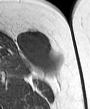
MRI of an extremity soft-tissue mass, one axial slice. Slice 21 of 45 in the series (ordered by position). MR volume resampled by the dataset authors to the PET/CT grid (not the native acquisition matrix). 90 × 109 image matrix, field of view 88 × 106 mm. Female patient. Case-level facts recorded for this patient, not image findings: histological type: leiomyosarcoma; grade: intermediate; site of the primary tumour: parascapusular.
Annotated regions visible in this slice (expert contour drawn on MRI and transferred to this co-registered scan by the dataset authors):
- gross tumour volume including surrounding oedema: box from (x=15, y=30) to (x=59, y=76) px
- gross tumour volume (mass): (x=17, y=30)–(x=54, y=74)